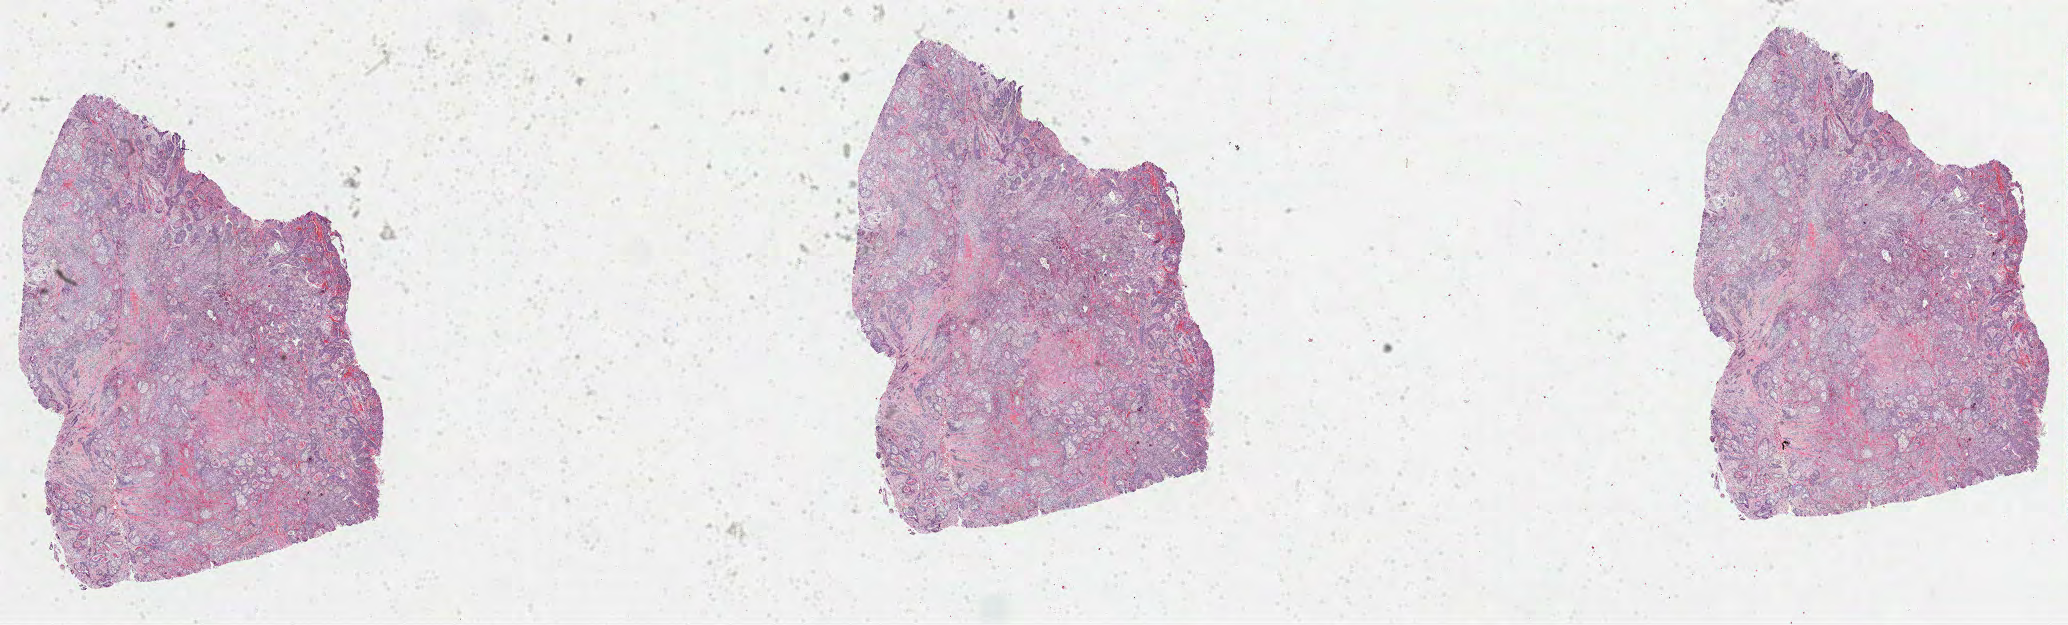
Whole-slide histology image, H&E, whole scanned area (about 33.4 x 10.1 mm, slide scanned at 40x) shown as a low-resolution overview. FFPE section. Primary tumour sample from the head and neck. Patient: female, age at initial diagnosis 63 years. Histologic grade: G3 (poorly differentiated).
Lymph nodes positive (case pathology): 3 of 52 examined. AJCC pathologic stage: IVA (7th edition). Diagnosis: Squamous cell carcinoma, NOS (overlapping lesion of lip, oral cavity and pharynx).